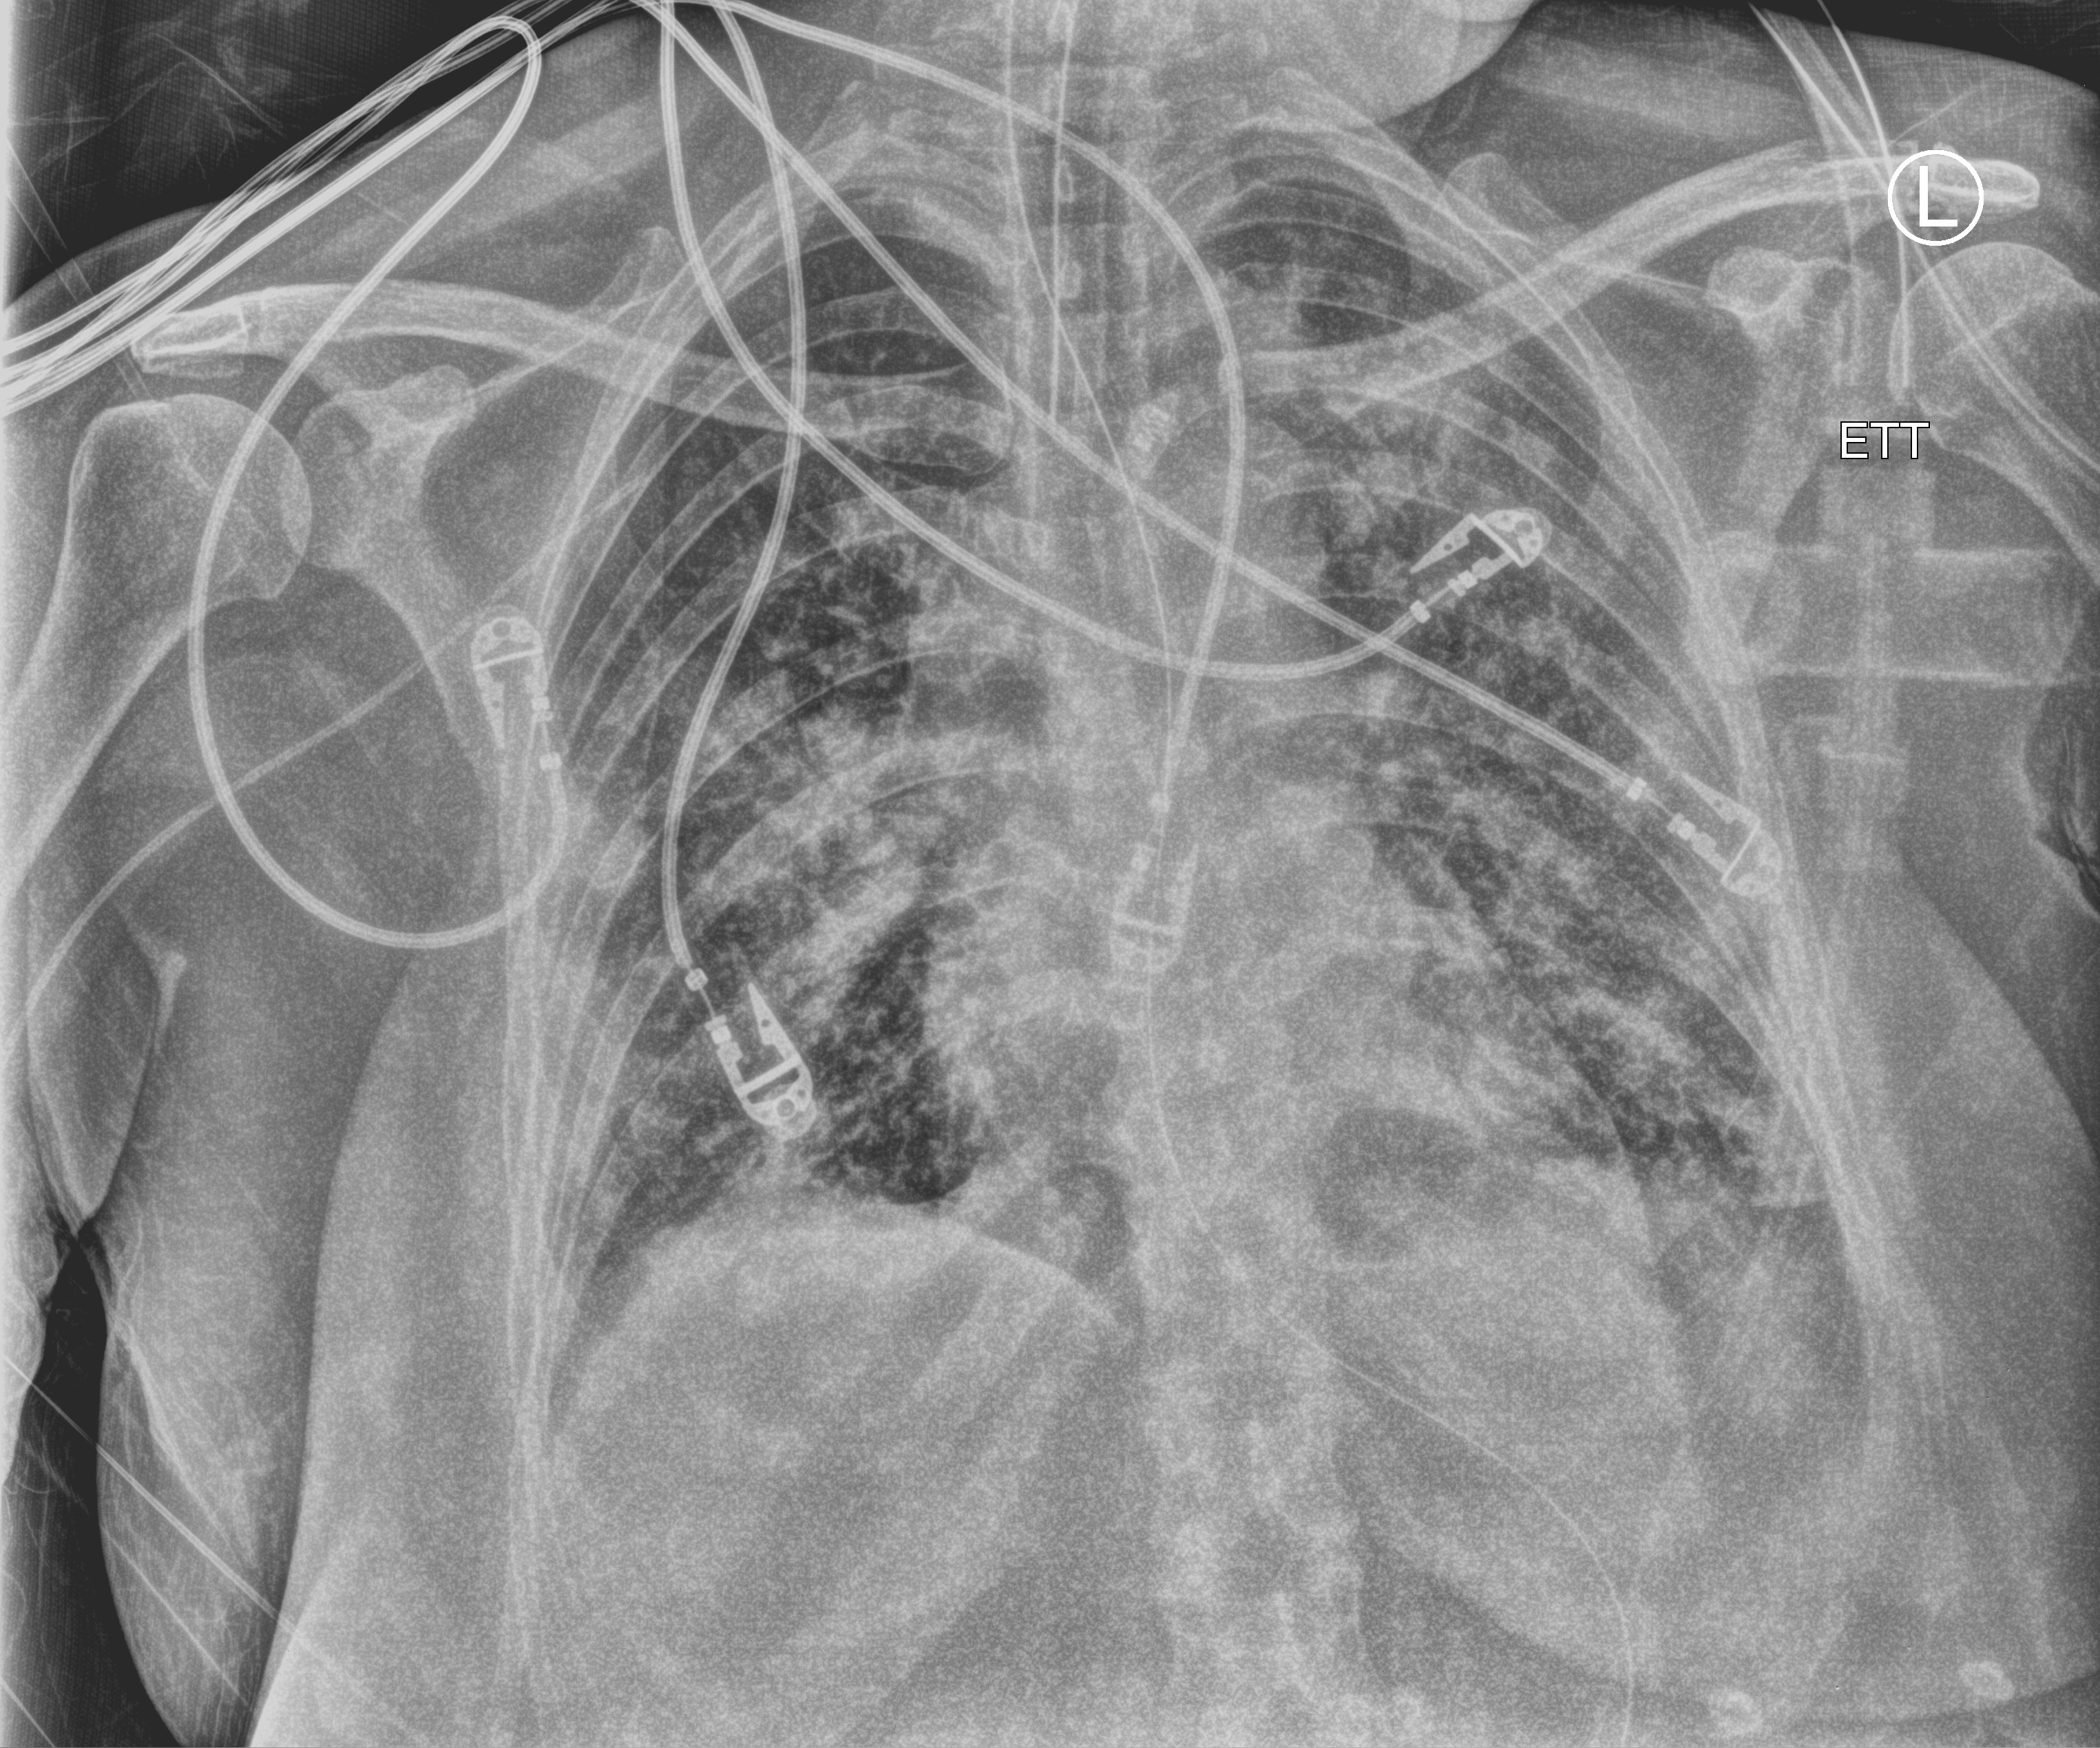
Chest X-ray (portable), anteroposterior (AP) projection. Patient hospitalised with COVID-19; female, aged 18–59 years.
From the hospital-stay record, not from the radiograph (when in the stay this image was taken is not recorded): length of hospital stay: 22 days; mechanically ventilated during this hospital stay: yes; admitted to intensive care during this hospital stay: yes.